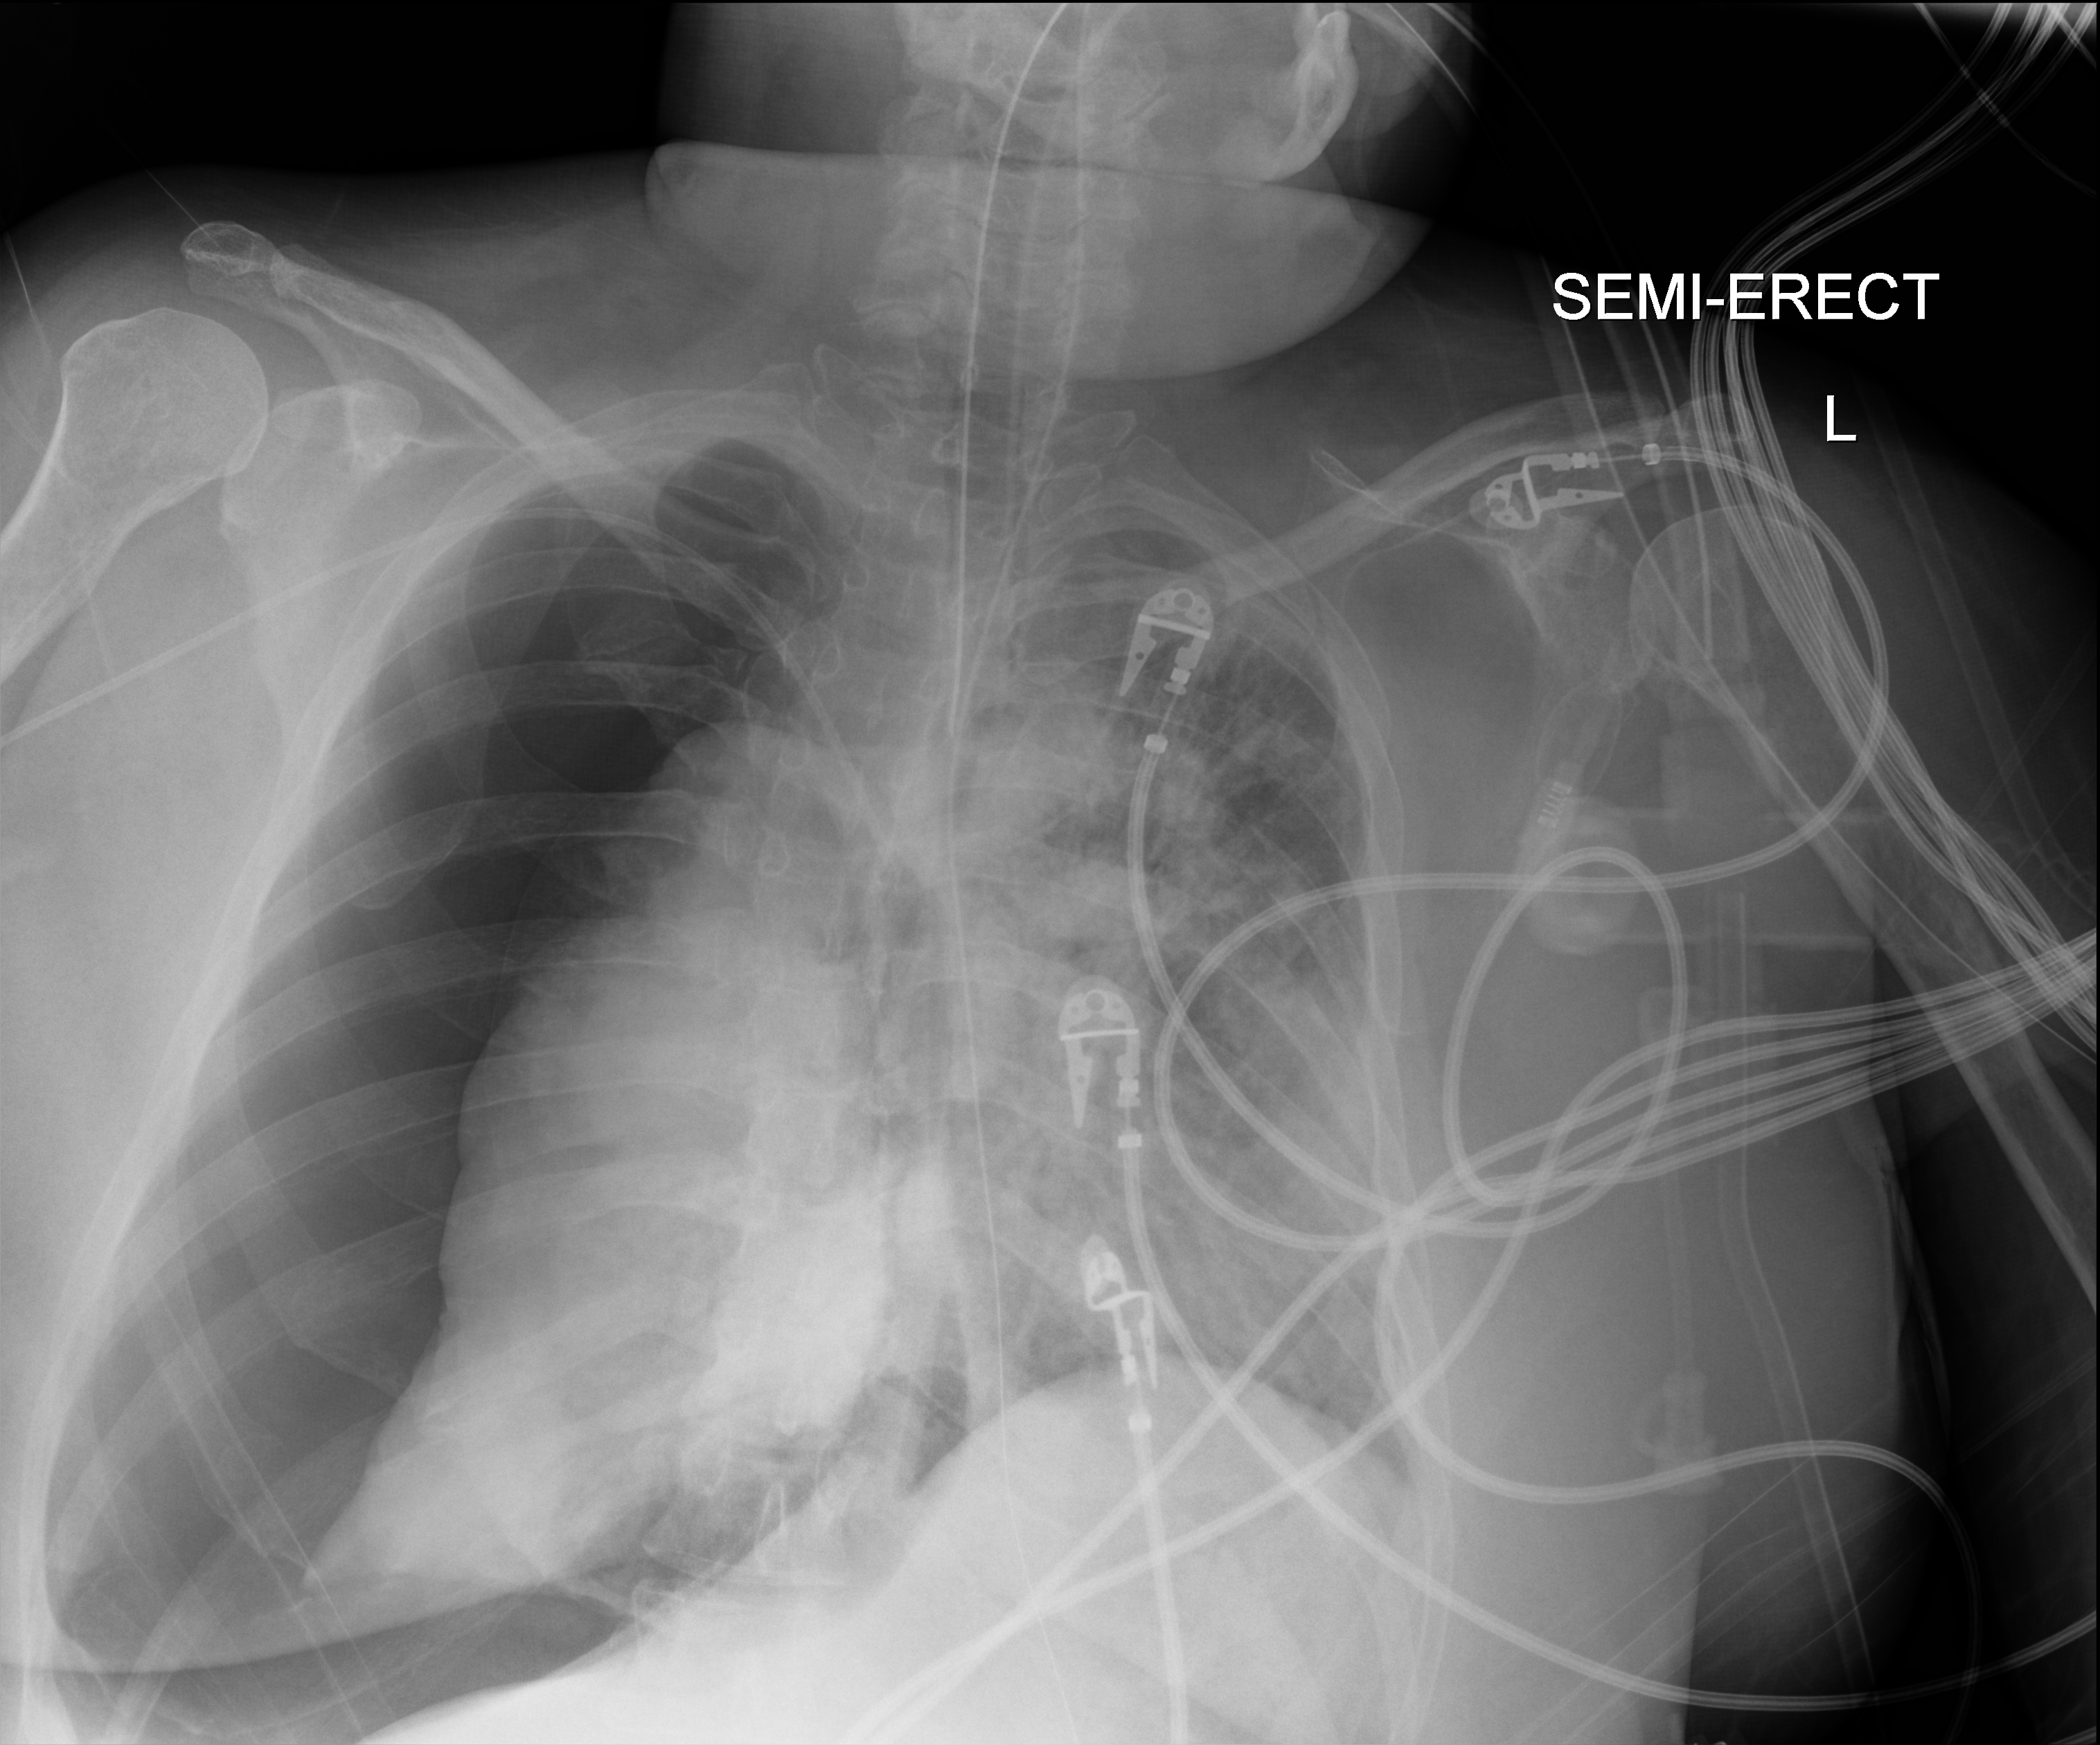
Chest X-ray (portable). Adult patient hospitalised with COVID-19, age 18–59 years.
Admission-level facts for this patient (not findings on this image; timing relative to this image not recorded):
- admitted to intensive care during this hospital stay: yes
- mechanically ventilated during this hospital stay: yes